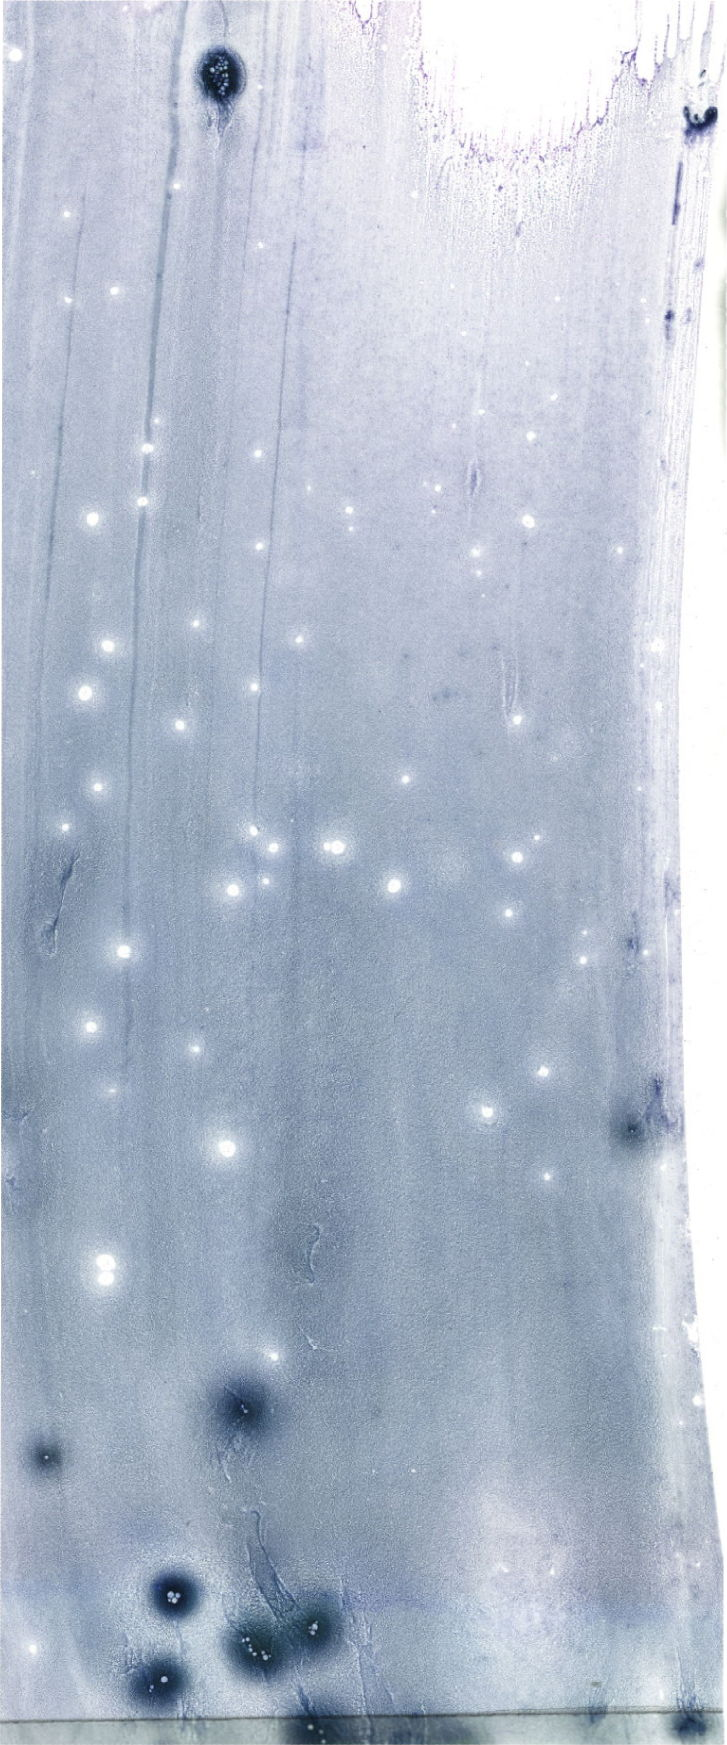
May-Grünwald-Giemsa (MGG)-stained marrow aspirate smear (whole slide), shown as a low-resolution overview of the whole scanned area (about 20.6 x 49.5 mm). Male patient.
Diagnosis: B Acute Lymphoblastic Leukemia.